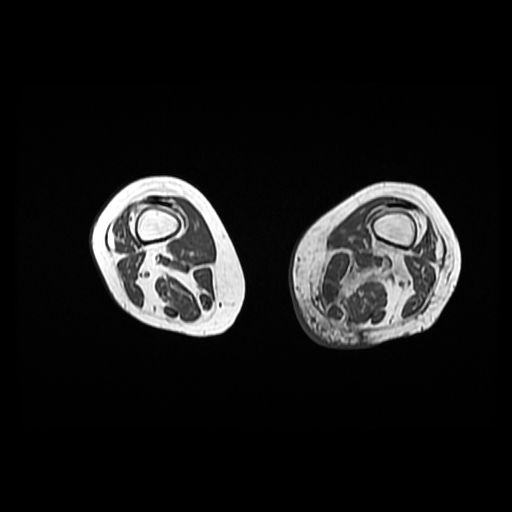
MRI of an extremity soft-tissue mass, one axial slice. Slice 19 of 42 in the series (ordered by position). 512 × 512 image matrix, field of view 420 × 420 mm. Female patient. Case-level facts recorded for this patient, not image findings: histological type: pleomorphic leiomyosarcoma; grade: high; site of the primary tumour: left thigh.
Structures marked on this image (manually delineated by an expert):
- gross tumour volume including surrounding oedema: bounding box [x1, y1, x2, y2] px = [319, 246, 407, 324]